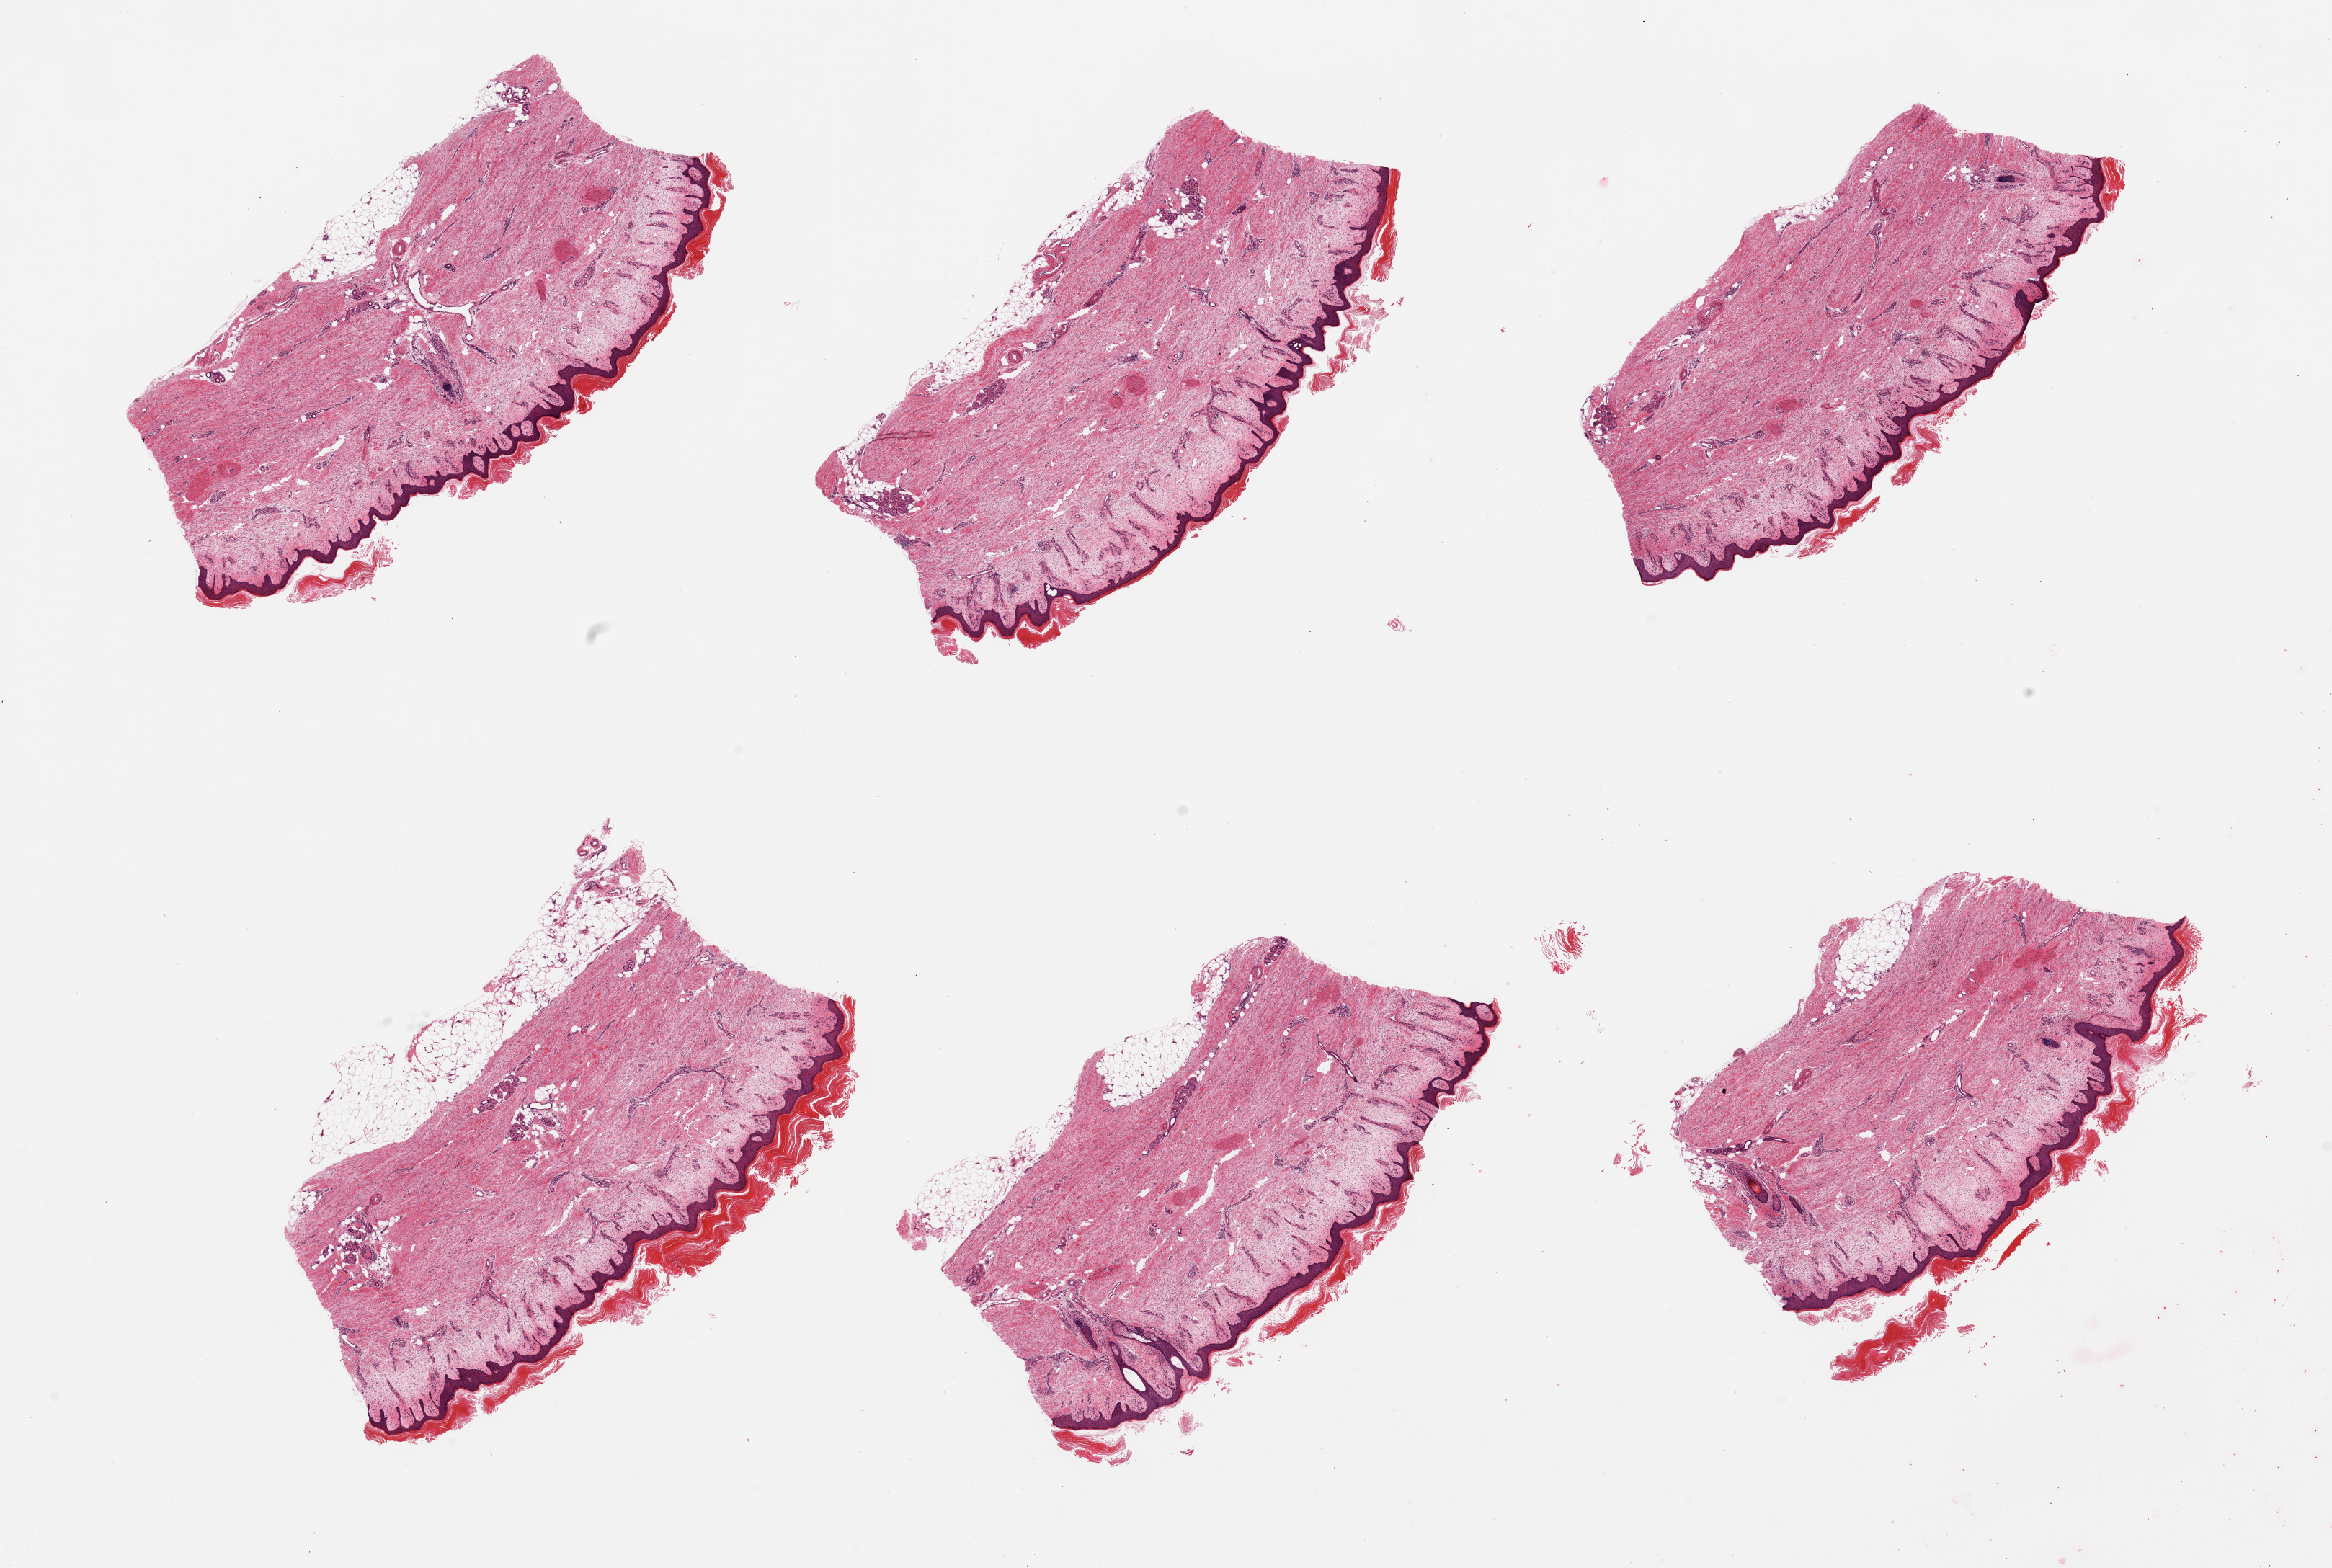
Whole-slide image, hematoxylin and eosin (H&E) stain, brightfield, low-resolution overview of the scanned area, about 25.6 x 17.2 mm (from a 20x scan). PAXgene-fixed, paraffin-embedded tissue. Section of skin of lower leg (target tissue). Tissue donor sample. Female donor.
• reviewer comment on this tissue sample: 6 pieces; dermal edema and hyperkeratosis; subcutaneous fat up to 0.5 mm thick